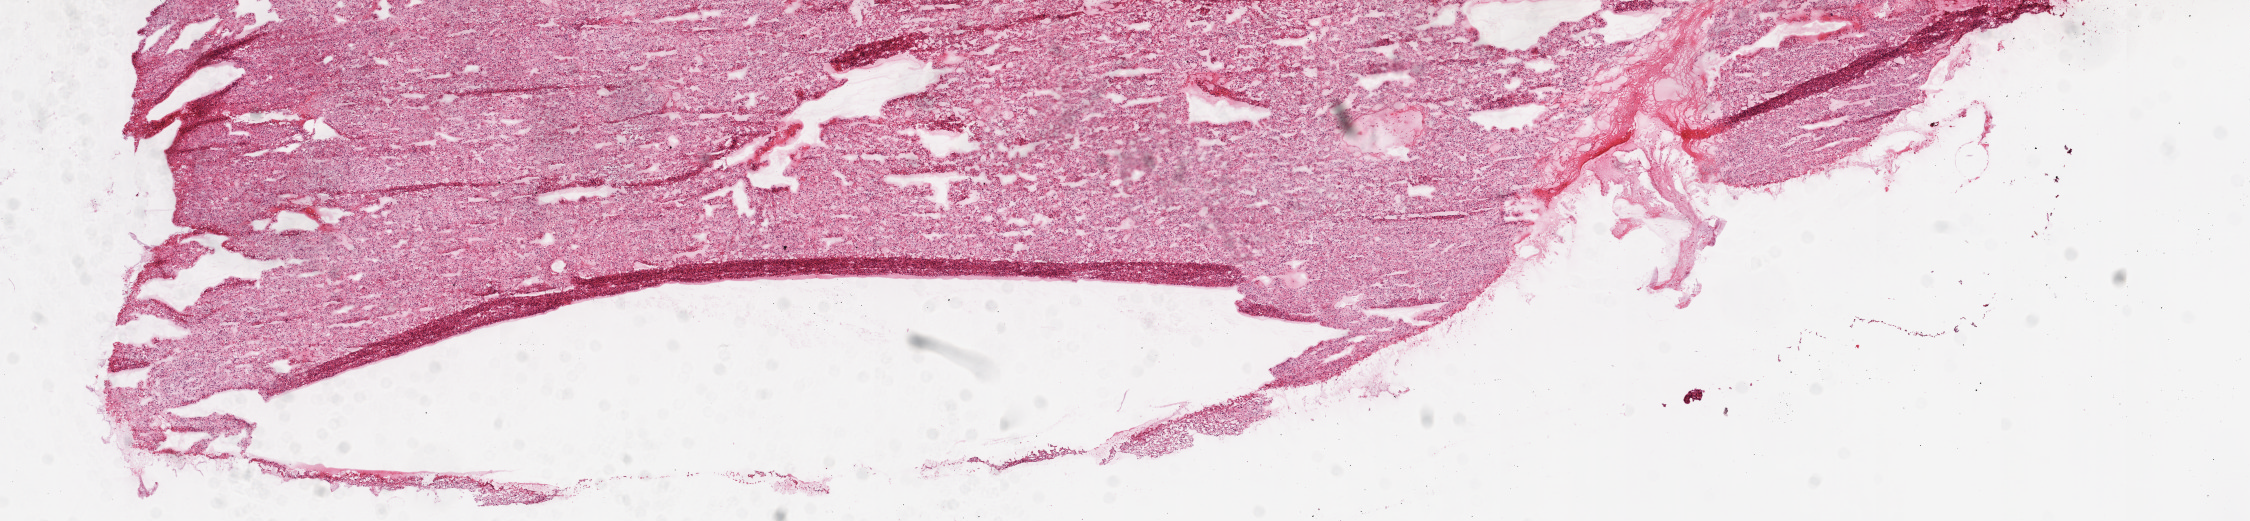
Whole-slide histology image, Hematoxylin and eosin (H&E) stained, shown as a low-resolution overview of the whole scanned area (about 18.1 x 4.2 mm, acquisition: 20x scan), frozen section from the top of the tissue portion, kidney, primary tumour sample. Female patient. Histologic grade: G2 (moderately differentiated). Slide review estimates, as recorded: tumour cells 95%, tumour nuclei 85%, normal cells 0%, stromal cells 5%, necrosis 0%.
Histologic diagnosis: Clear cell adenocarcinoma, NOS. AJCC pathologic stage: I. TNM: T1 N0 M0.